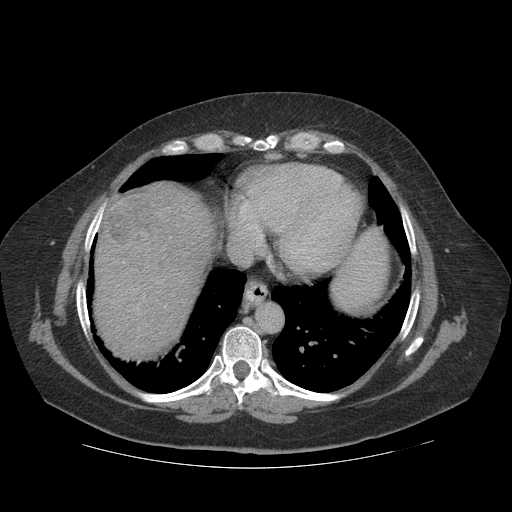
Contrast-enhanced abdominal CT (liver protocol), one axial slice. Reconstruction kernel STANDARD. Soft-tissue window (W 400 / L 40 HU). 2.5 mm slice thickness. 512 × 512 image matrix. Case-level facts recorded for this patient, not image findings: diagnosis: hepatocellular carcinoma (patient treated with transarterial chemoembolisation; whether this scan precedes or follows treatment is not stated here); TNM stage (as recorded): Stage-IIIA; Child-Pugh class: A; tumour nodularity: multinodular.
Outlined on this slice (semi-automatically segmented with operator editing):
- liver parenchyma outside the tumour (the mass and vessels are separate outlines, so this box may not span the whole liver): bounding box (x1, y1, x2, y2) in pixels: (94, 182, 212, 356)
- mass: (103, 194, 158, 246)